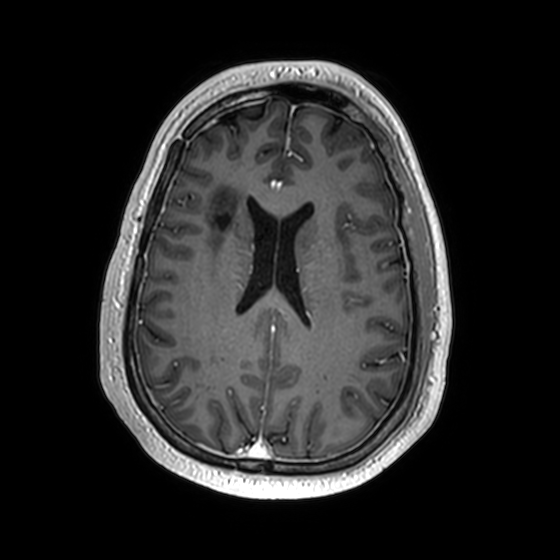
Brain MRI from a brain-tumour surgery series, one axial slice; position 71 of 174 along the scan axis; T1-weighted post-contrast; 560 × 560 image matrix. Case-level facts recorded for this patient, not image findings: histopathology: Astrocytoma; WHO grade: 2; IDH mutation: yes; tumour location: Right Insular.
Annotated regions visible in this slice (outlined manually by an expert reader):
- previous resection cavity: box from (x=217, y=214) to (x=230, y=229) px